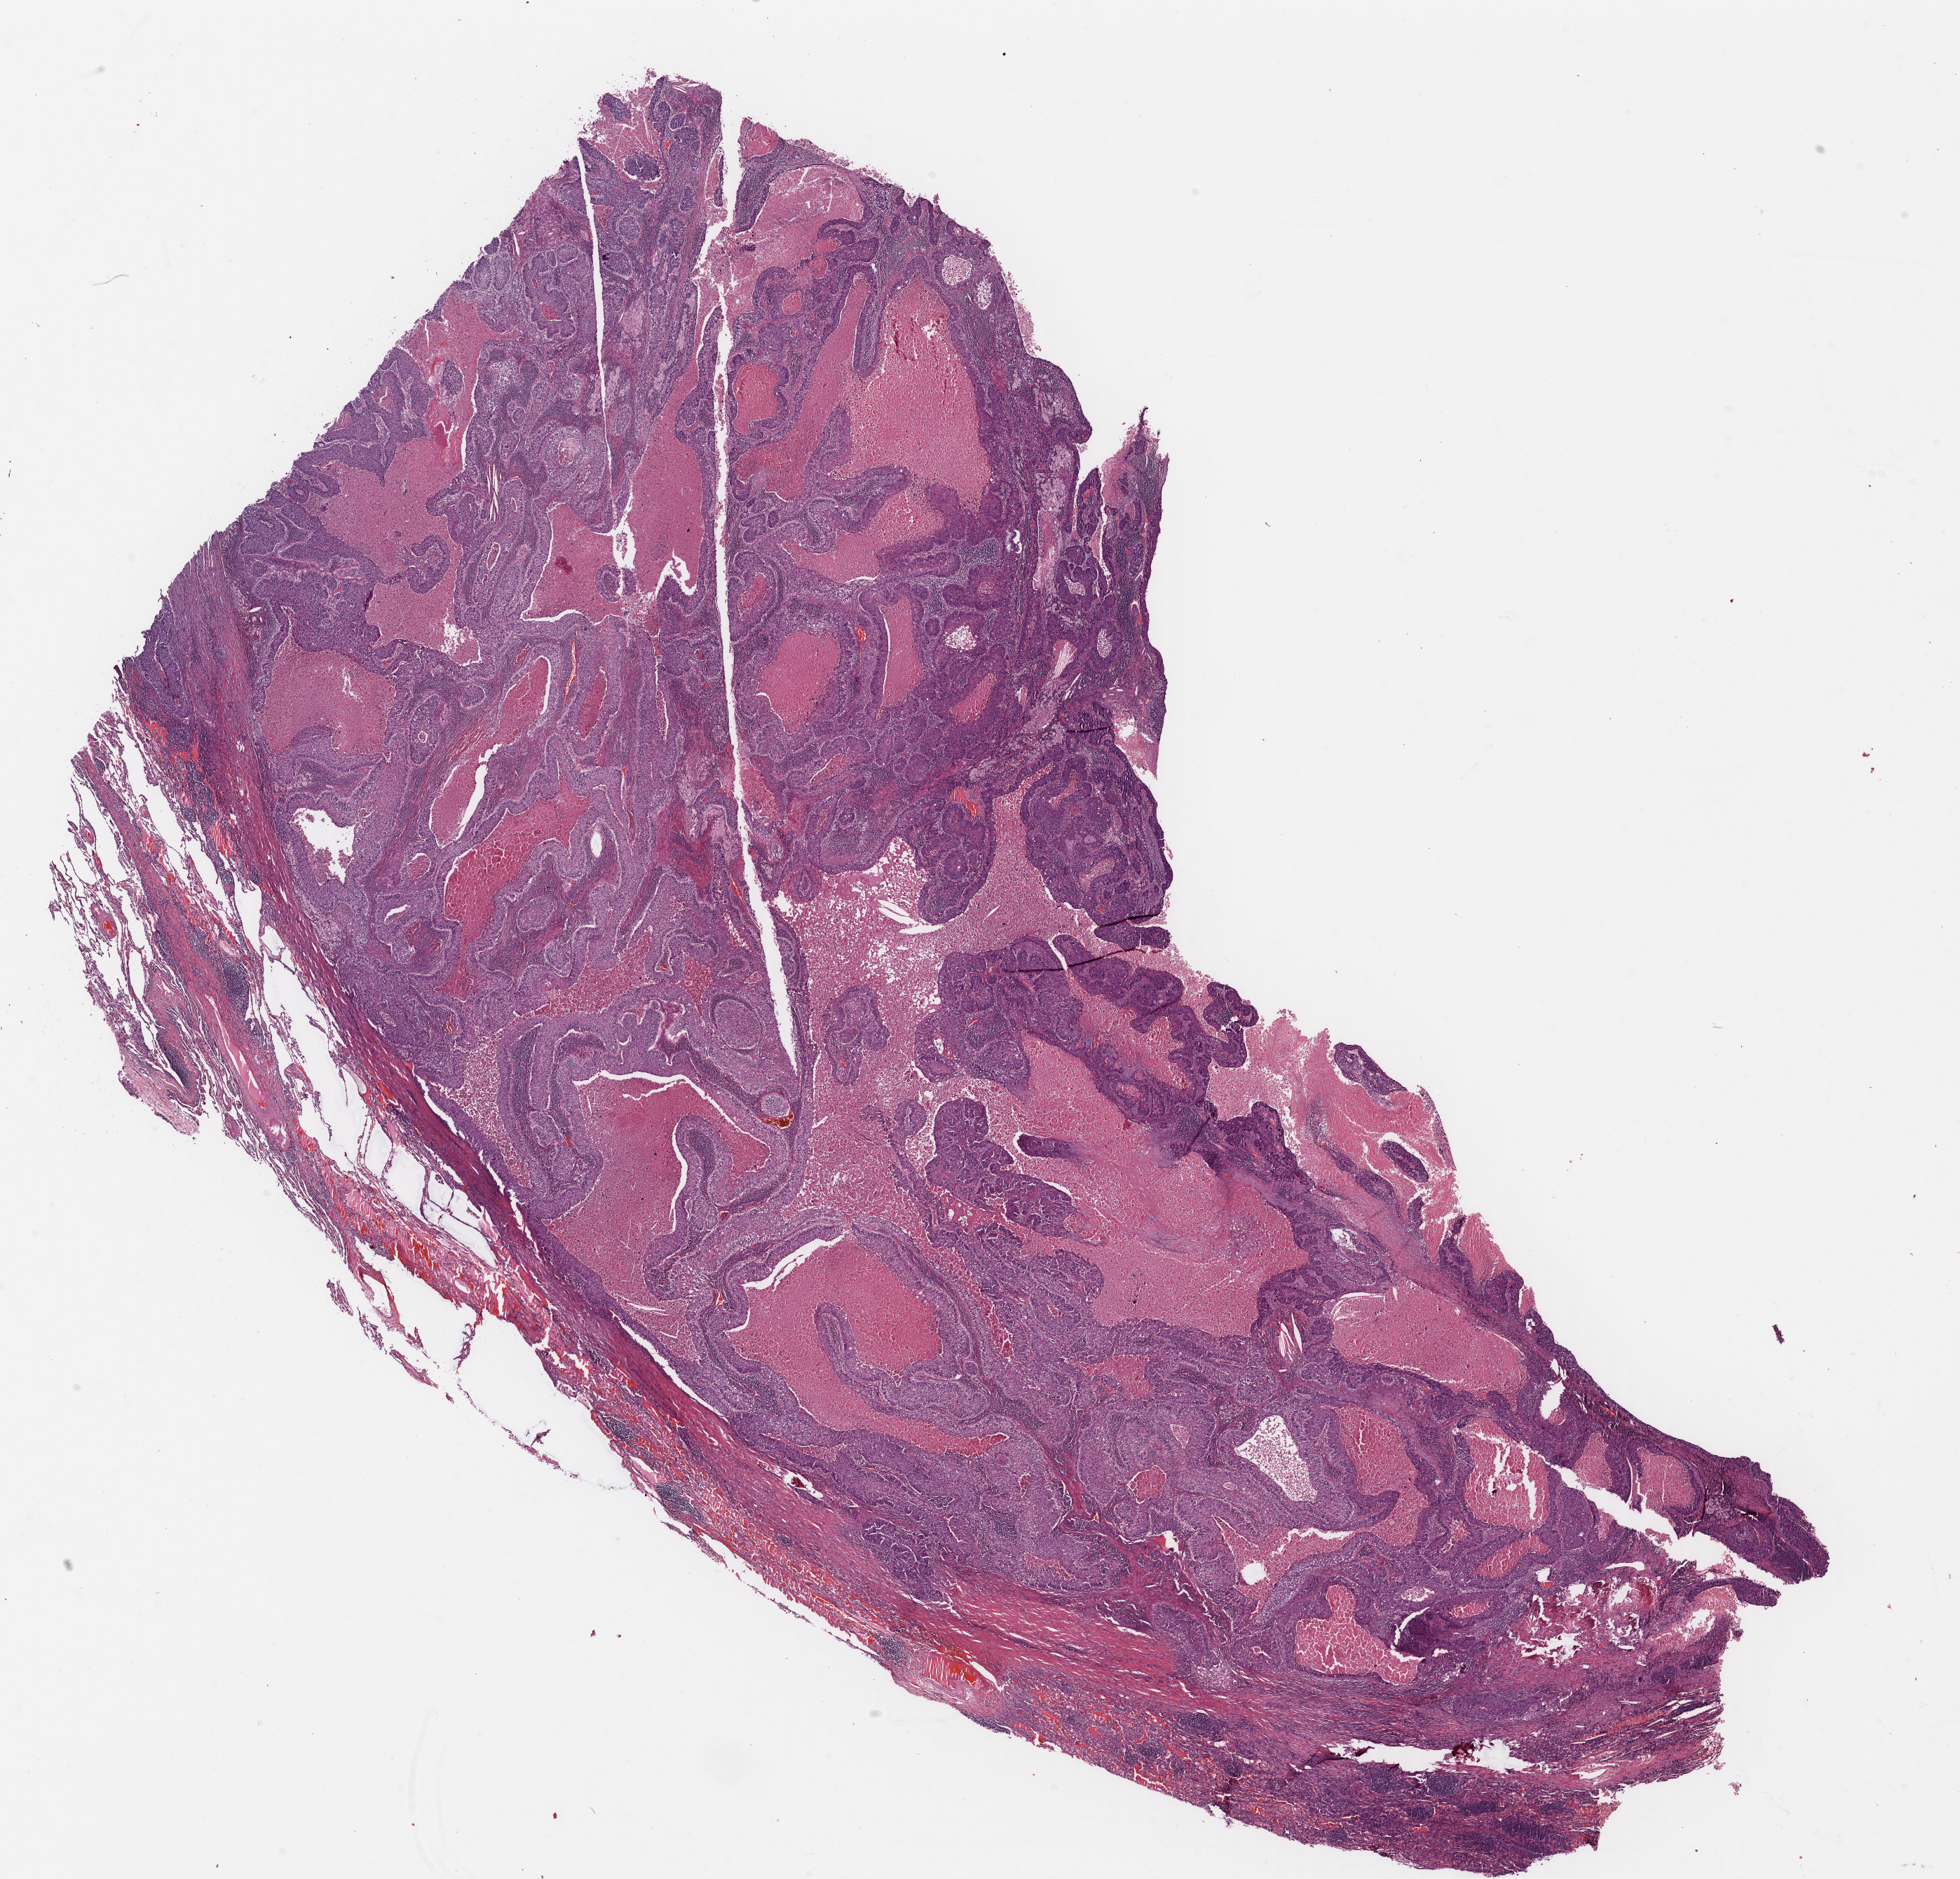
Whole-slide histology image, H&E-stained — shown as a low-resolution overview of the whole scanned area (about 22.0 x 21.1 mm, from a 40x scan), formalin-fixed paraffin-embedded (FFPE) diagnostic section, primary tumour sample from the lung. Male patient; age at initial diagnosis 70 years.
Pathologic diagnosis: Squamous cell carcinoma, NOS.